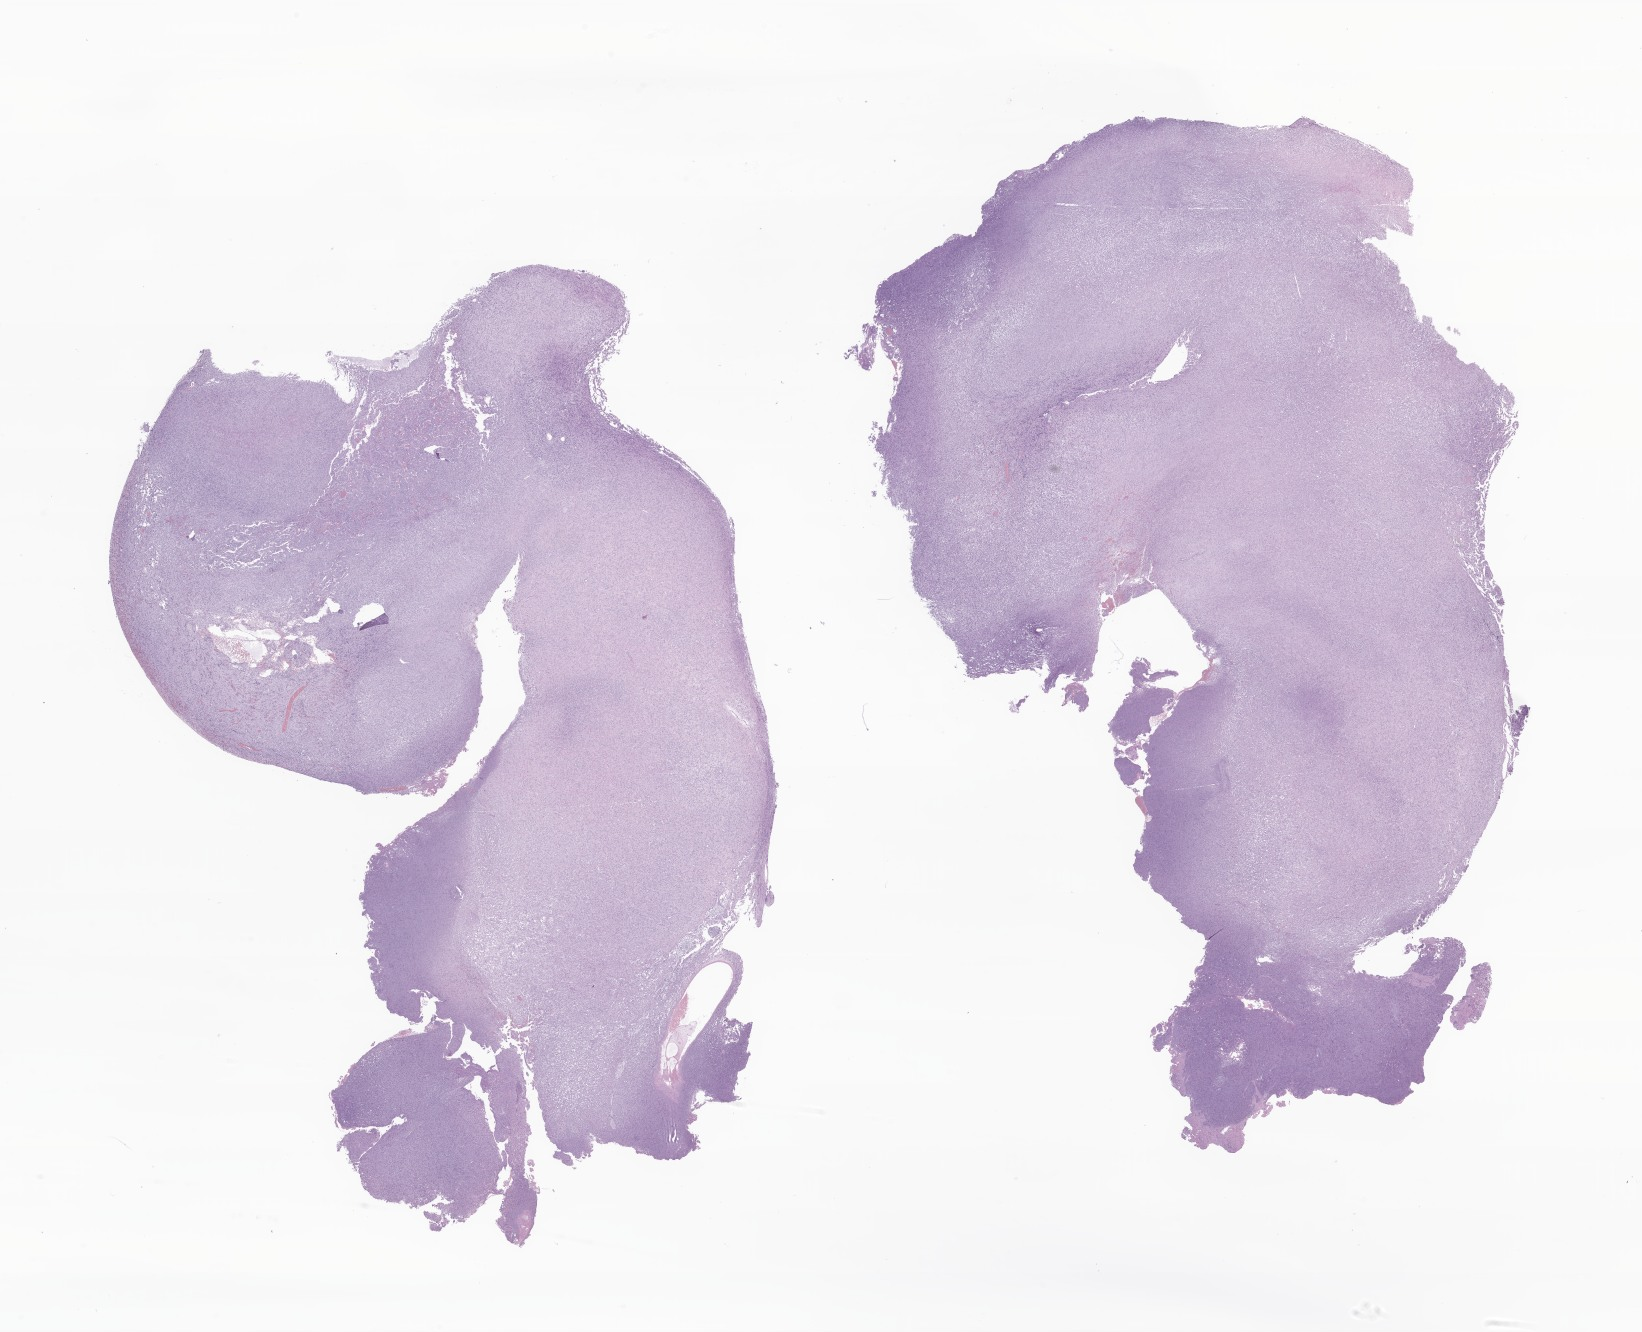
Digitized H&E-stained section of tumor tissue from the brain, a low-resolution overview of the entire scanned area, about 27.7 x 22.5 mm; FFPE section. Patient male; age 158 days.
Recorded diagnosis: Glioma, malignant.